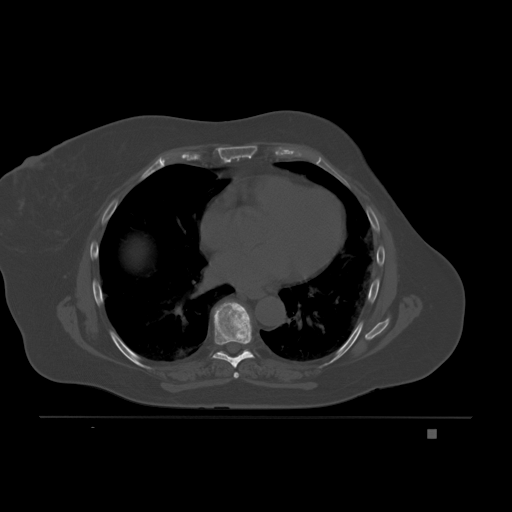
CT including the spine, one axial slice; position 126 of 221 along the scan axis; bone window (W 1800 / L 400 HU); 3 mm slice thickness; 512 × 512 image matrix, field of view 474 × 474 mm. Patient: female, 63 years. From the clinical record (not read from this slice): primary cancer: breast.
Annotated regions visible in this slice (semi-automatically segmented with operator editing):
- T6 vertebra: box from (x=234, y=372) to (x=239, y=379) px
- T7 vertebra: (x=212, y=302)–(x=255, y=368)
- T8 vertebra: (x=220, y=349)–(x=247, y=353)